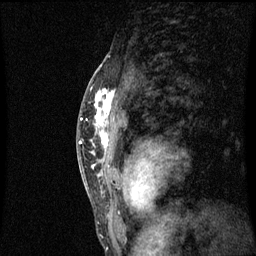
Breast MRI (dynamic contrast-enhanced), one sagittal slice. Position 41 of 60 along the scan axis. Dynamic contrast-enhanced series, image 2 of 3 at this slice position (ordered by acquisition). 1.5 T. TE 4.2 ms, TR 8.9 ms. 2 mm slice thickness. 256 × 256 image matrix, field of view 200 × 200 mm. Female patient, age 50 years. Case-level facts recorded for this patient, not image findings: setting: breast cancer imaged before/during neoadjuvant chemotherapy; receptor status: triple-negative.
Annotated regions visible in this slice (semi-automatically segmented with operator editing):
- analysis volume of interest (the breast-tissue region the enhancement analysis was run in; not a lesion): box from (x=84, y=80) to (x=121, y=171) px
- tumour enhancement mask (voxels above the 70 % enhancement threshold inside the analysis volume of interest): (x=92, y=90)–(x=115, y=167)